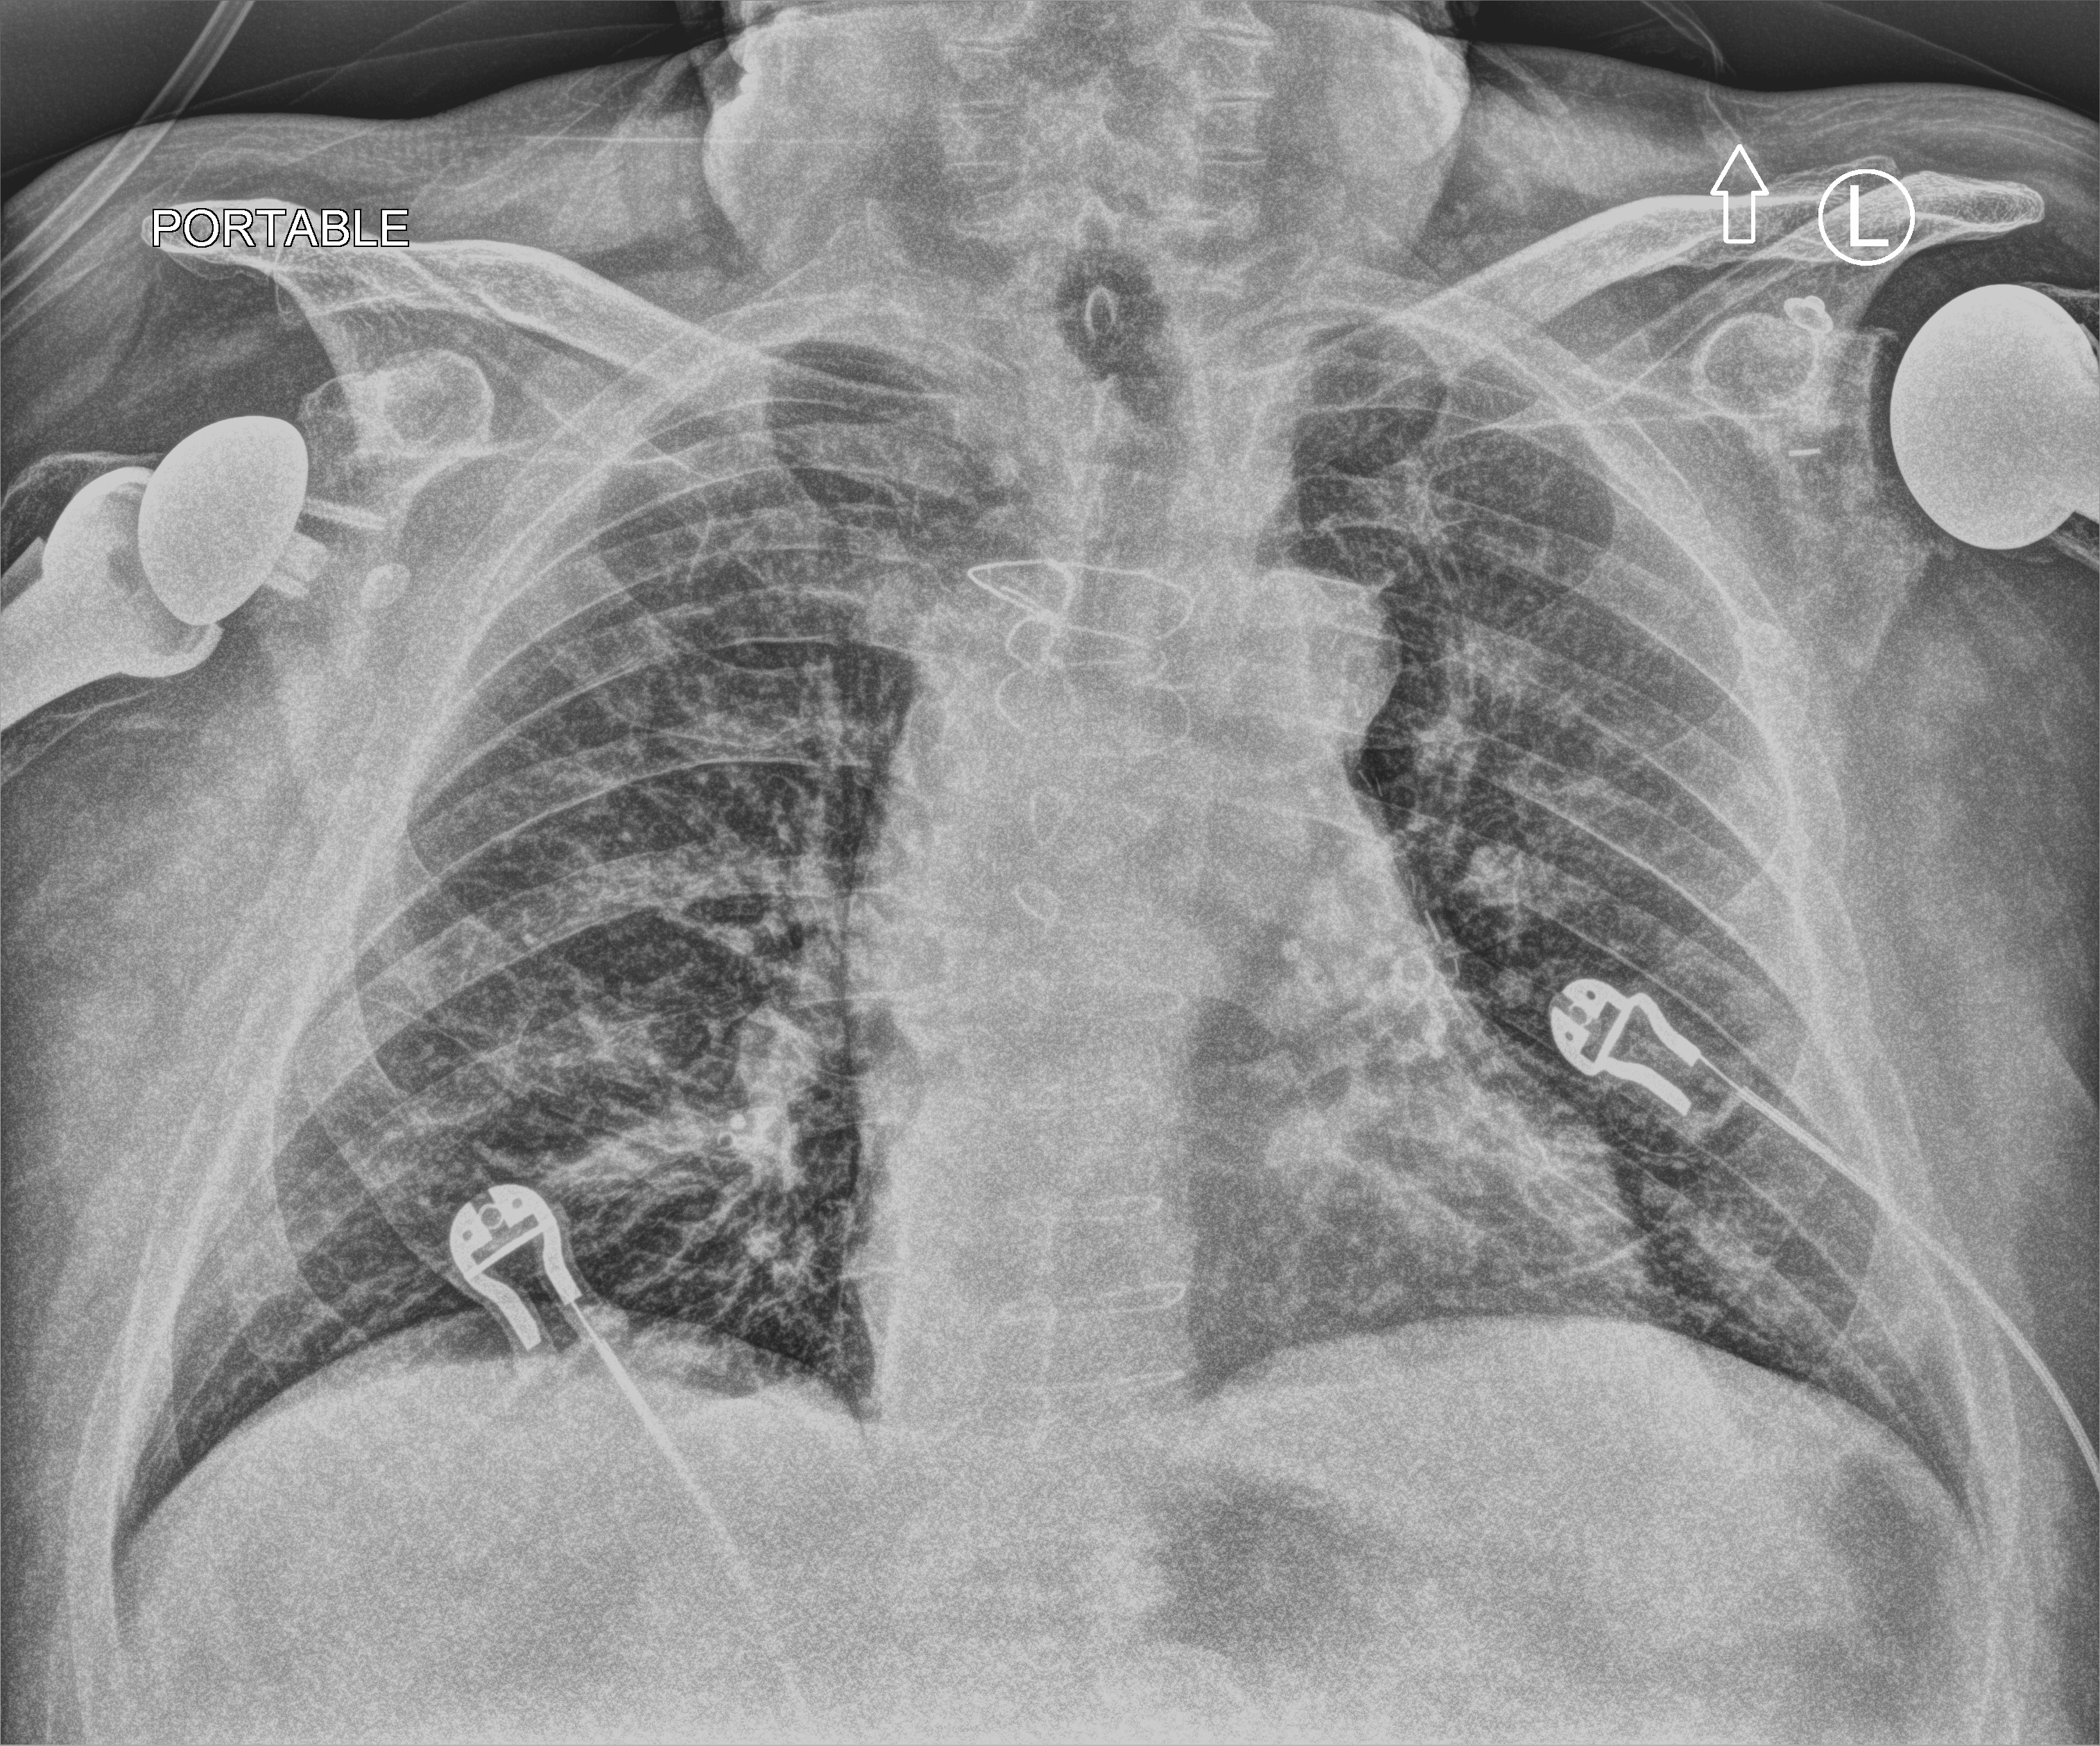
Chest X-ray (portable). Male patient hospitalised with COVID-19, age 60–74 years.
From the hospital-stay record, not from the radiograph (when in the stay this image was taken is not recorded): smoking status (admission record): never; mechanically ventilated during this hospital stay: no; COPD (admission record): no.